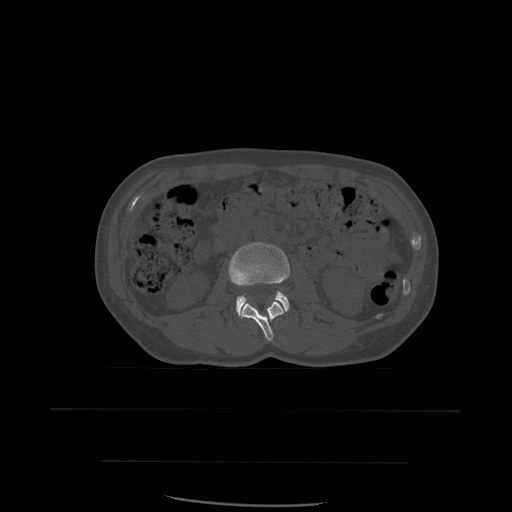
CT including the spine, one axial slice; slice 211 of 574 in the series (ordered by position); bone window (W 1800 / L 400 HU); 1.25 mm slice thickness; 512 × 512 image matrix, field of view 392 × 392 mm. Patient age 48 years. From the clinical record (not read from this slice): primary cancer: lung; vertebrae with lytic lesions (as recorded): T11.
Outlined on this slice (semi-automatically segmented with operator editing):
- L2 vertebra: bounding box [x1, y1, x2, y2] px = [239, 302, 285, 342]
- L3 vertebra: [229, 242, 290, 315]